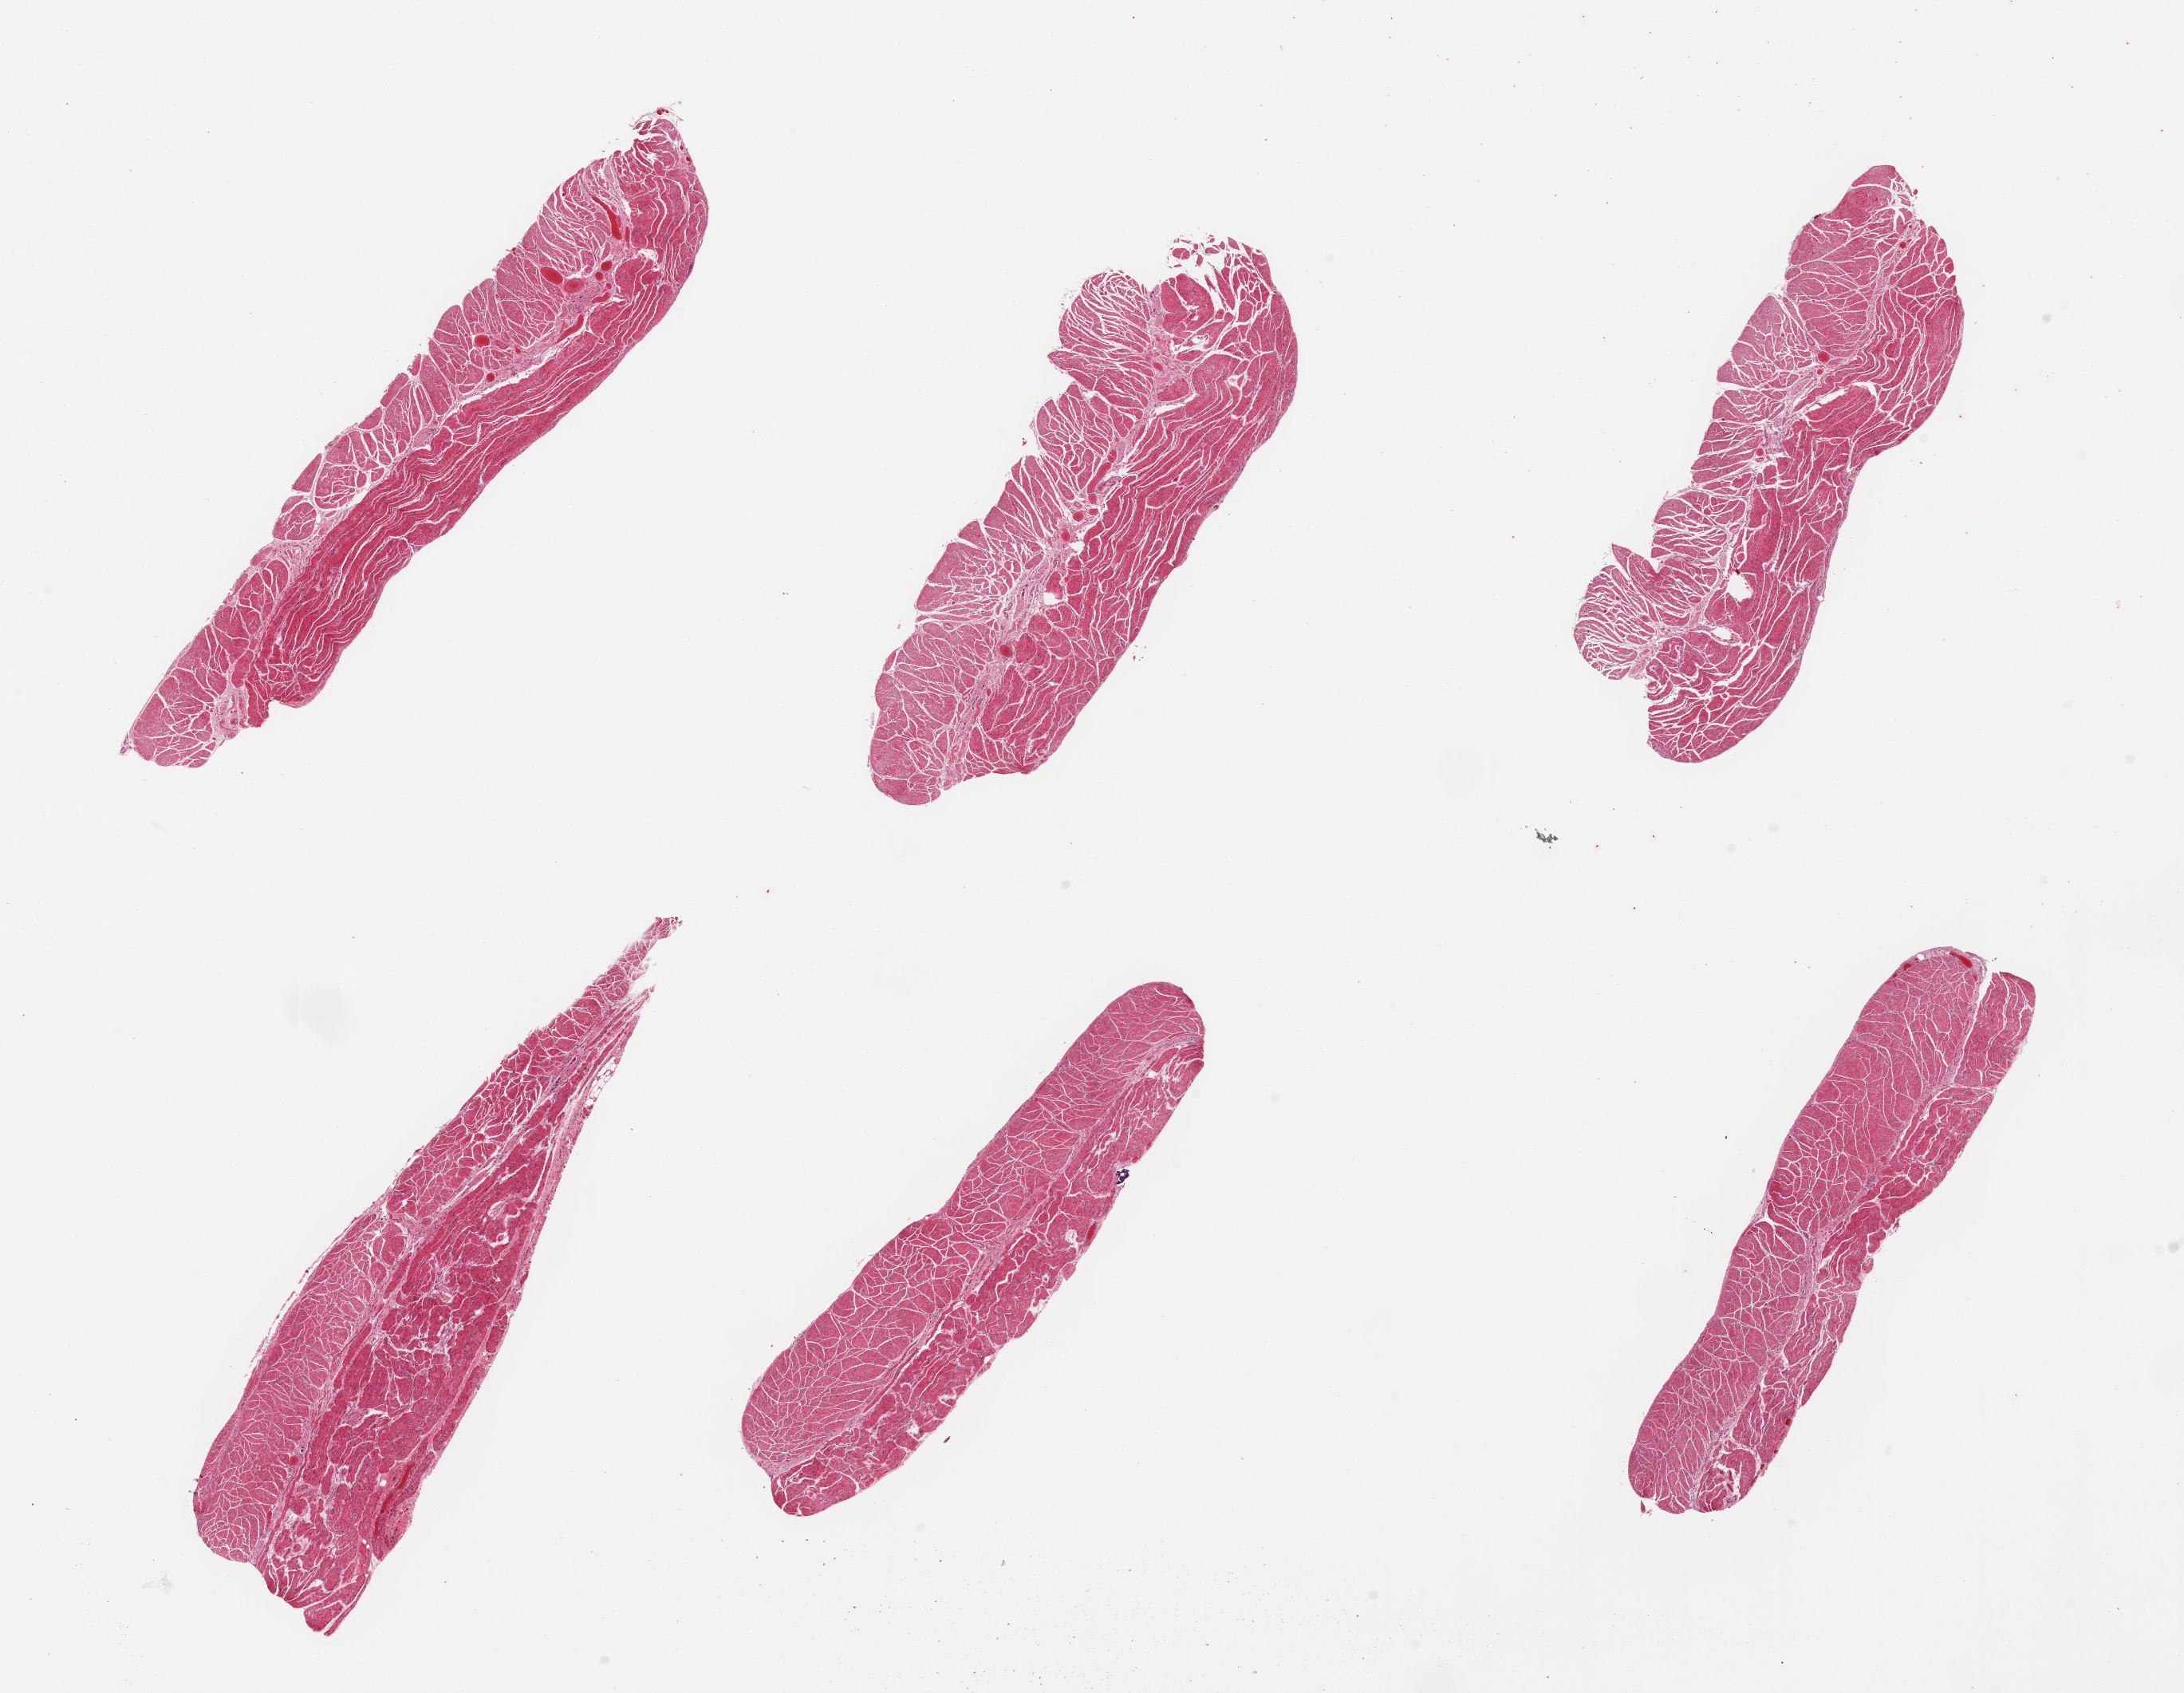
Digitized H&E-stained section, low-resolution overview of the scanned area, about 21.7 x 16.8 mm (slide scanned at 20x); PAXgene-fixed, paraffin-embedded tissue; section of esophageal muscle (target tissue); tissue donor sample. Donor: female.
Reviewer comment on this tissue sample: 6 pieces; well dissected muscle.